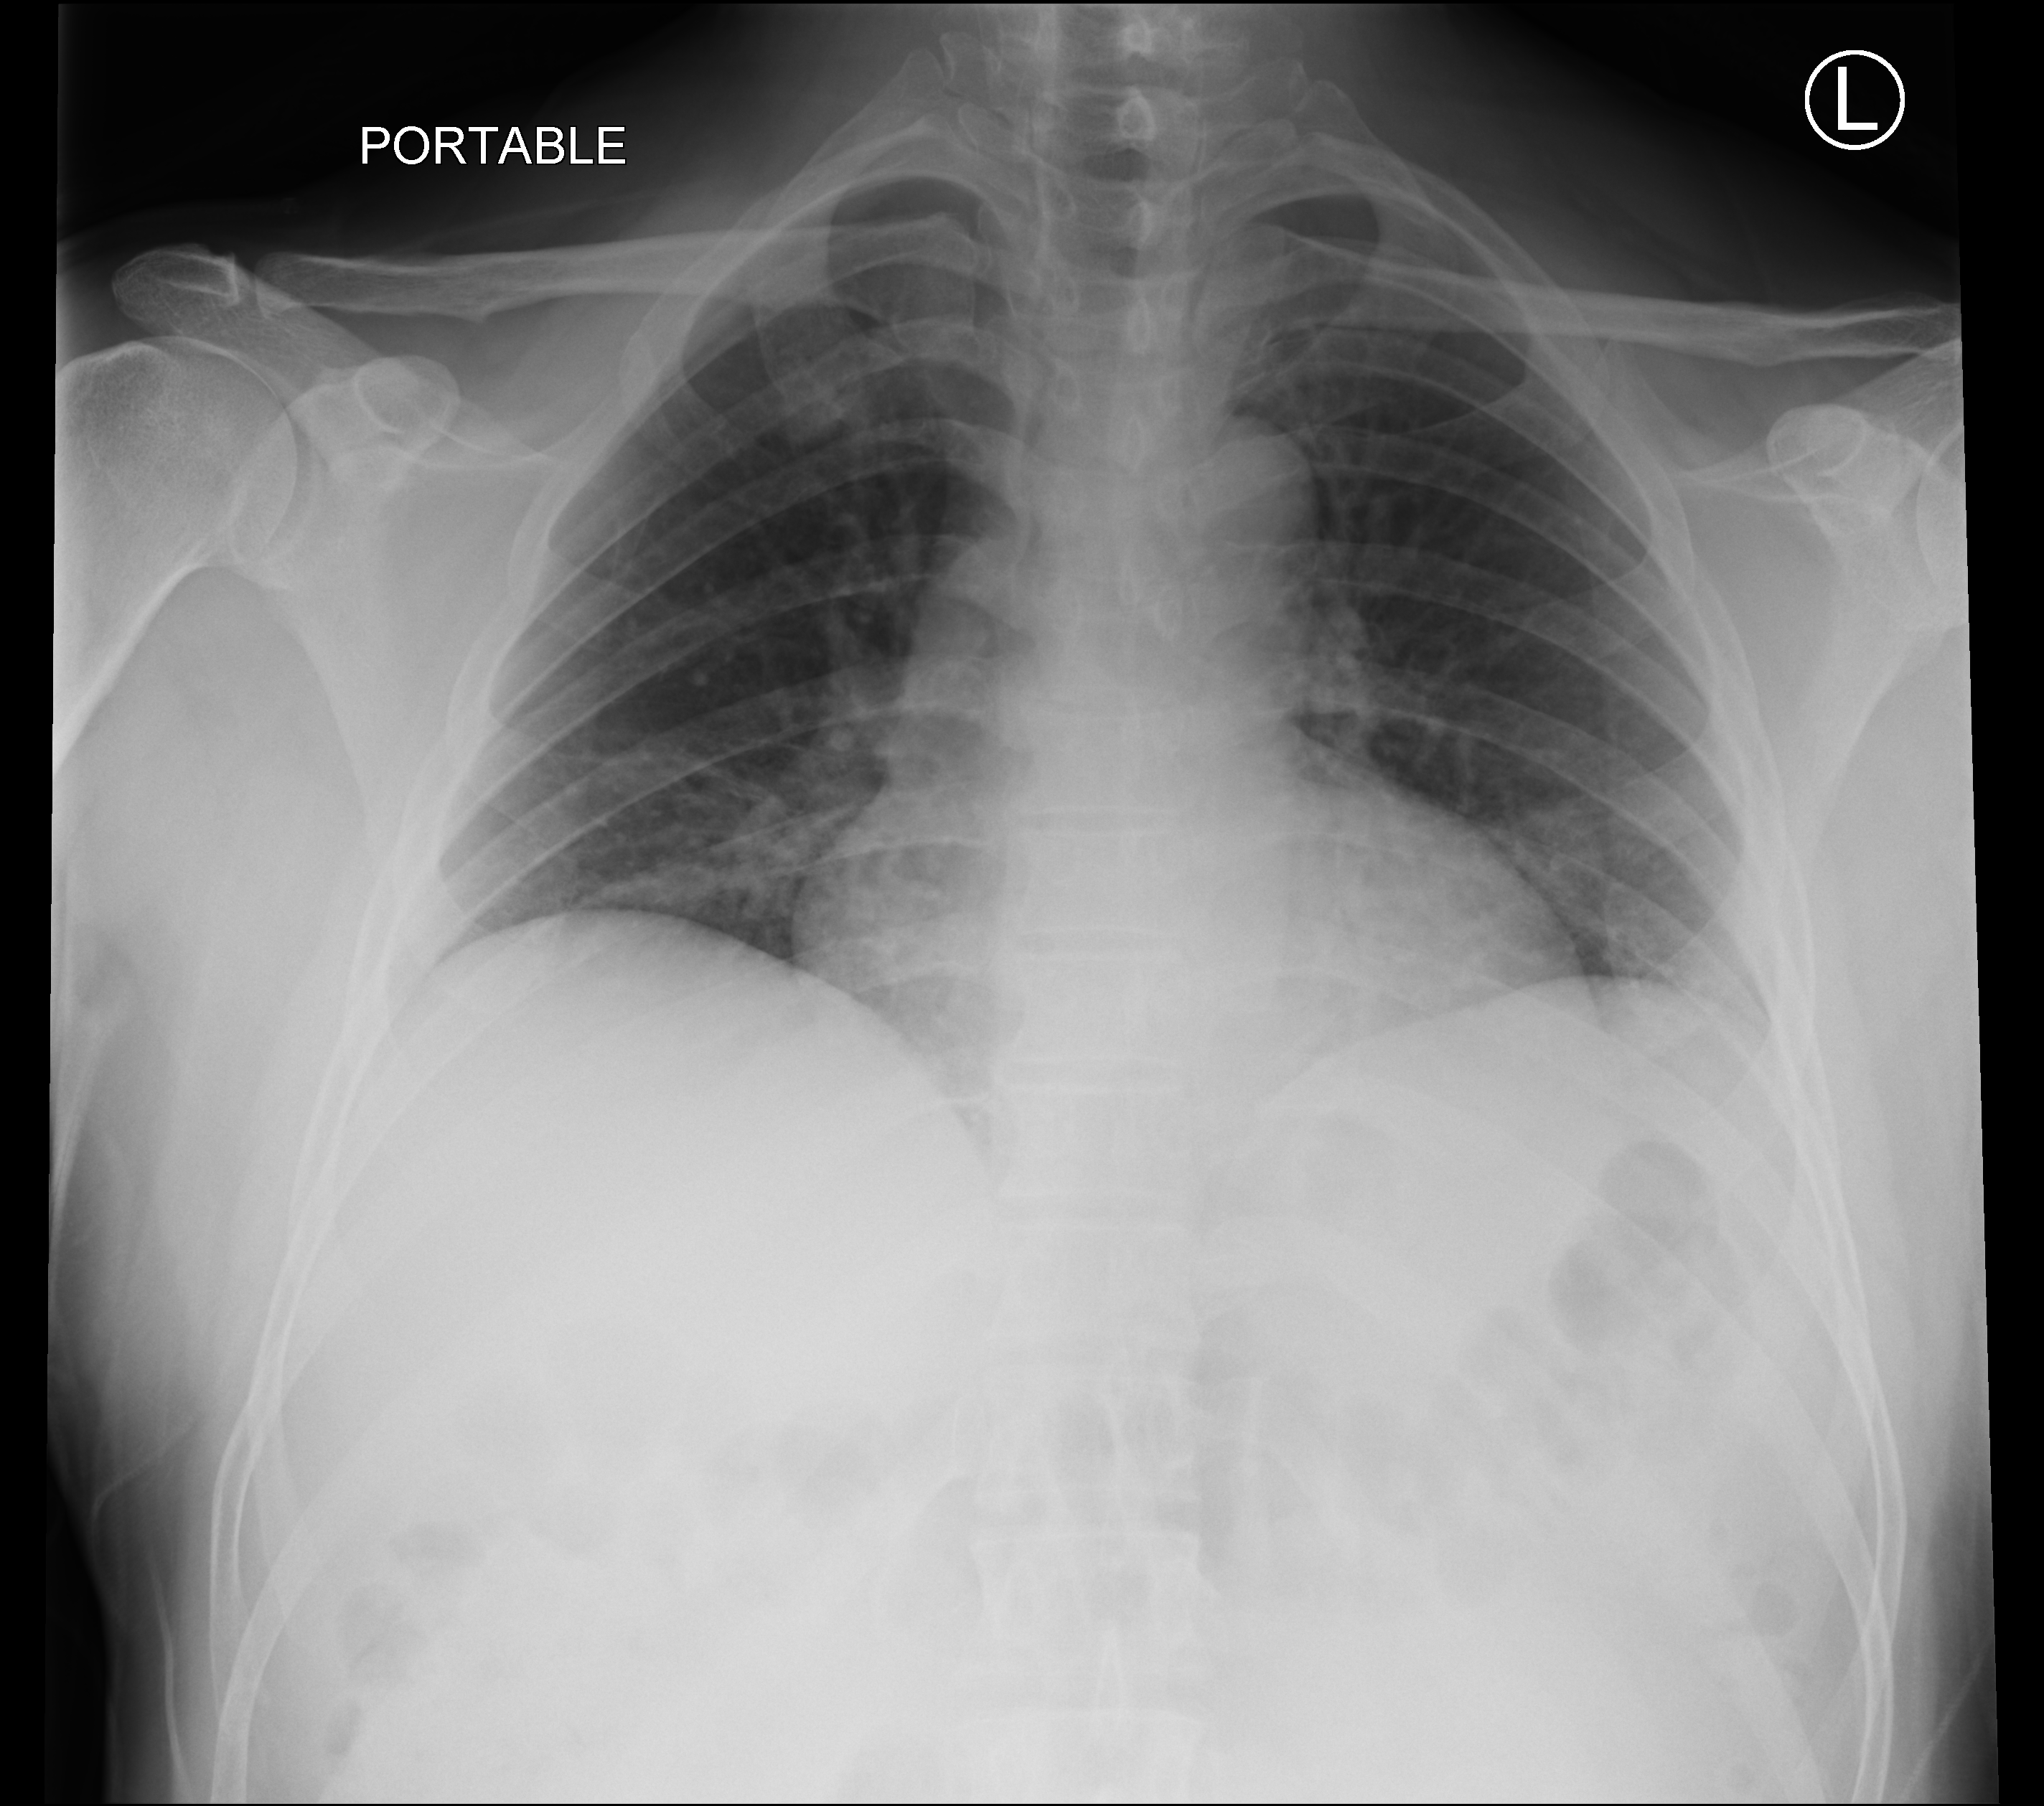
Portable chest radiograph. Male patient hospitalised with COVID-19, age 18–59 years.
From the hospital-stay record, not from the radiograph (when in the stay this image was taken is not recorded): chronic kidney disease (admission record): no; smoking status (admission record): never.